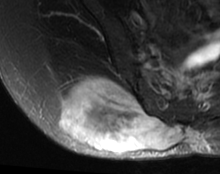
MRI of an extremity soft-tissue mass, one axial slice; slice 35 of 63 in the series (ordered by position); T2-weighted fat-saturated; MR volume resampled by the dataset authors to the PET/CT grid (not the native acquisition matrix); 3.27 mm slice thickness; 220 × 174 image matrix, field of view 215 × 170 mm. Female patient. From the clinical record (not read from this slice): histological type: spindle cell suggestive of myxofibrosarcoma; grade: intermediate; site of the primary tumour: right buttock.
Annotated regions visible in this slice (expert contour drawn on MRI and transferred to this co-registered scan by the dataset authors):
- gross tumour volume (mass): bounding box (x1, y1, x2, y2) in pixels: (59, 79, 183, 153)